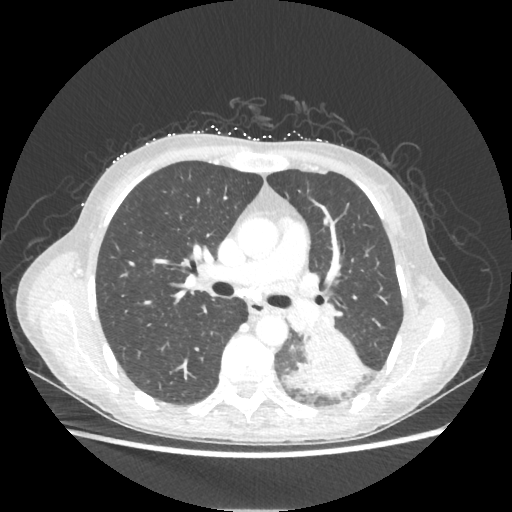
Chest CT, one axial slice; position 128 of 221 along the scan axis; lung window (W 1500 / L -600 HU); 1.25 mm slice thickness; 512 × 512 image matrix, field of view 360 × 360 mm. Female patient, age 53 years. Case-level facts recorded for this patient, not image findings: clinical TNM (as recorded): T3 N0 M0.
Structures marked on this image (rectangle marked by the reading radiologist):
- lung tumour (recorded histology: adenocarcinoma): box from (x=286, y=333) to (x=369, y=398) px